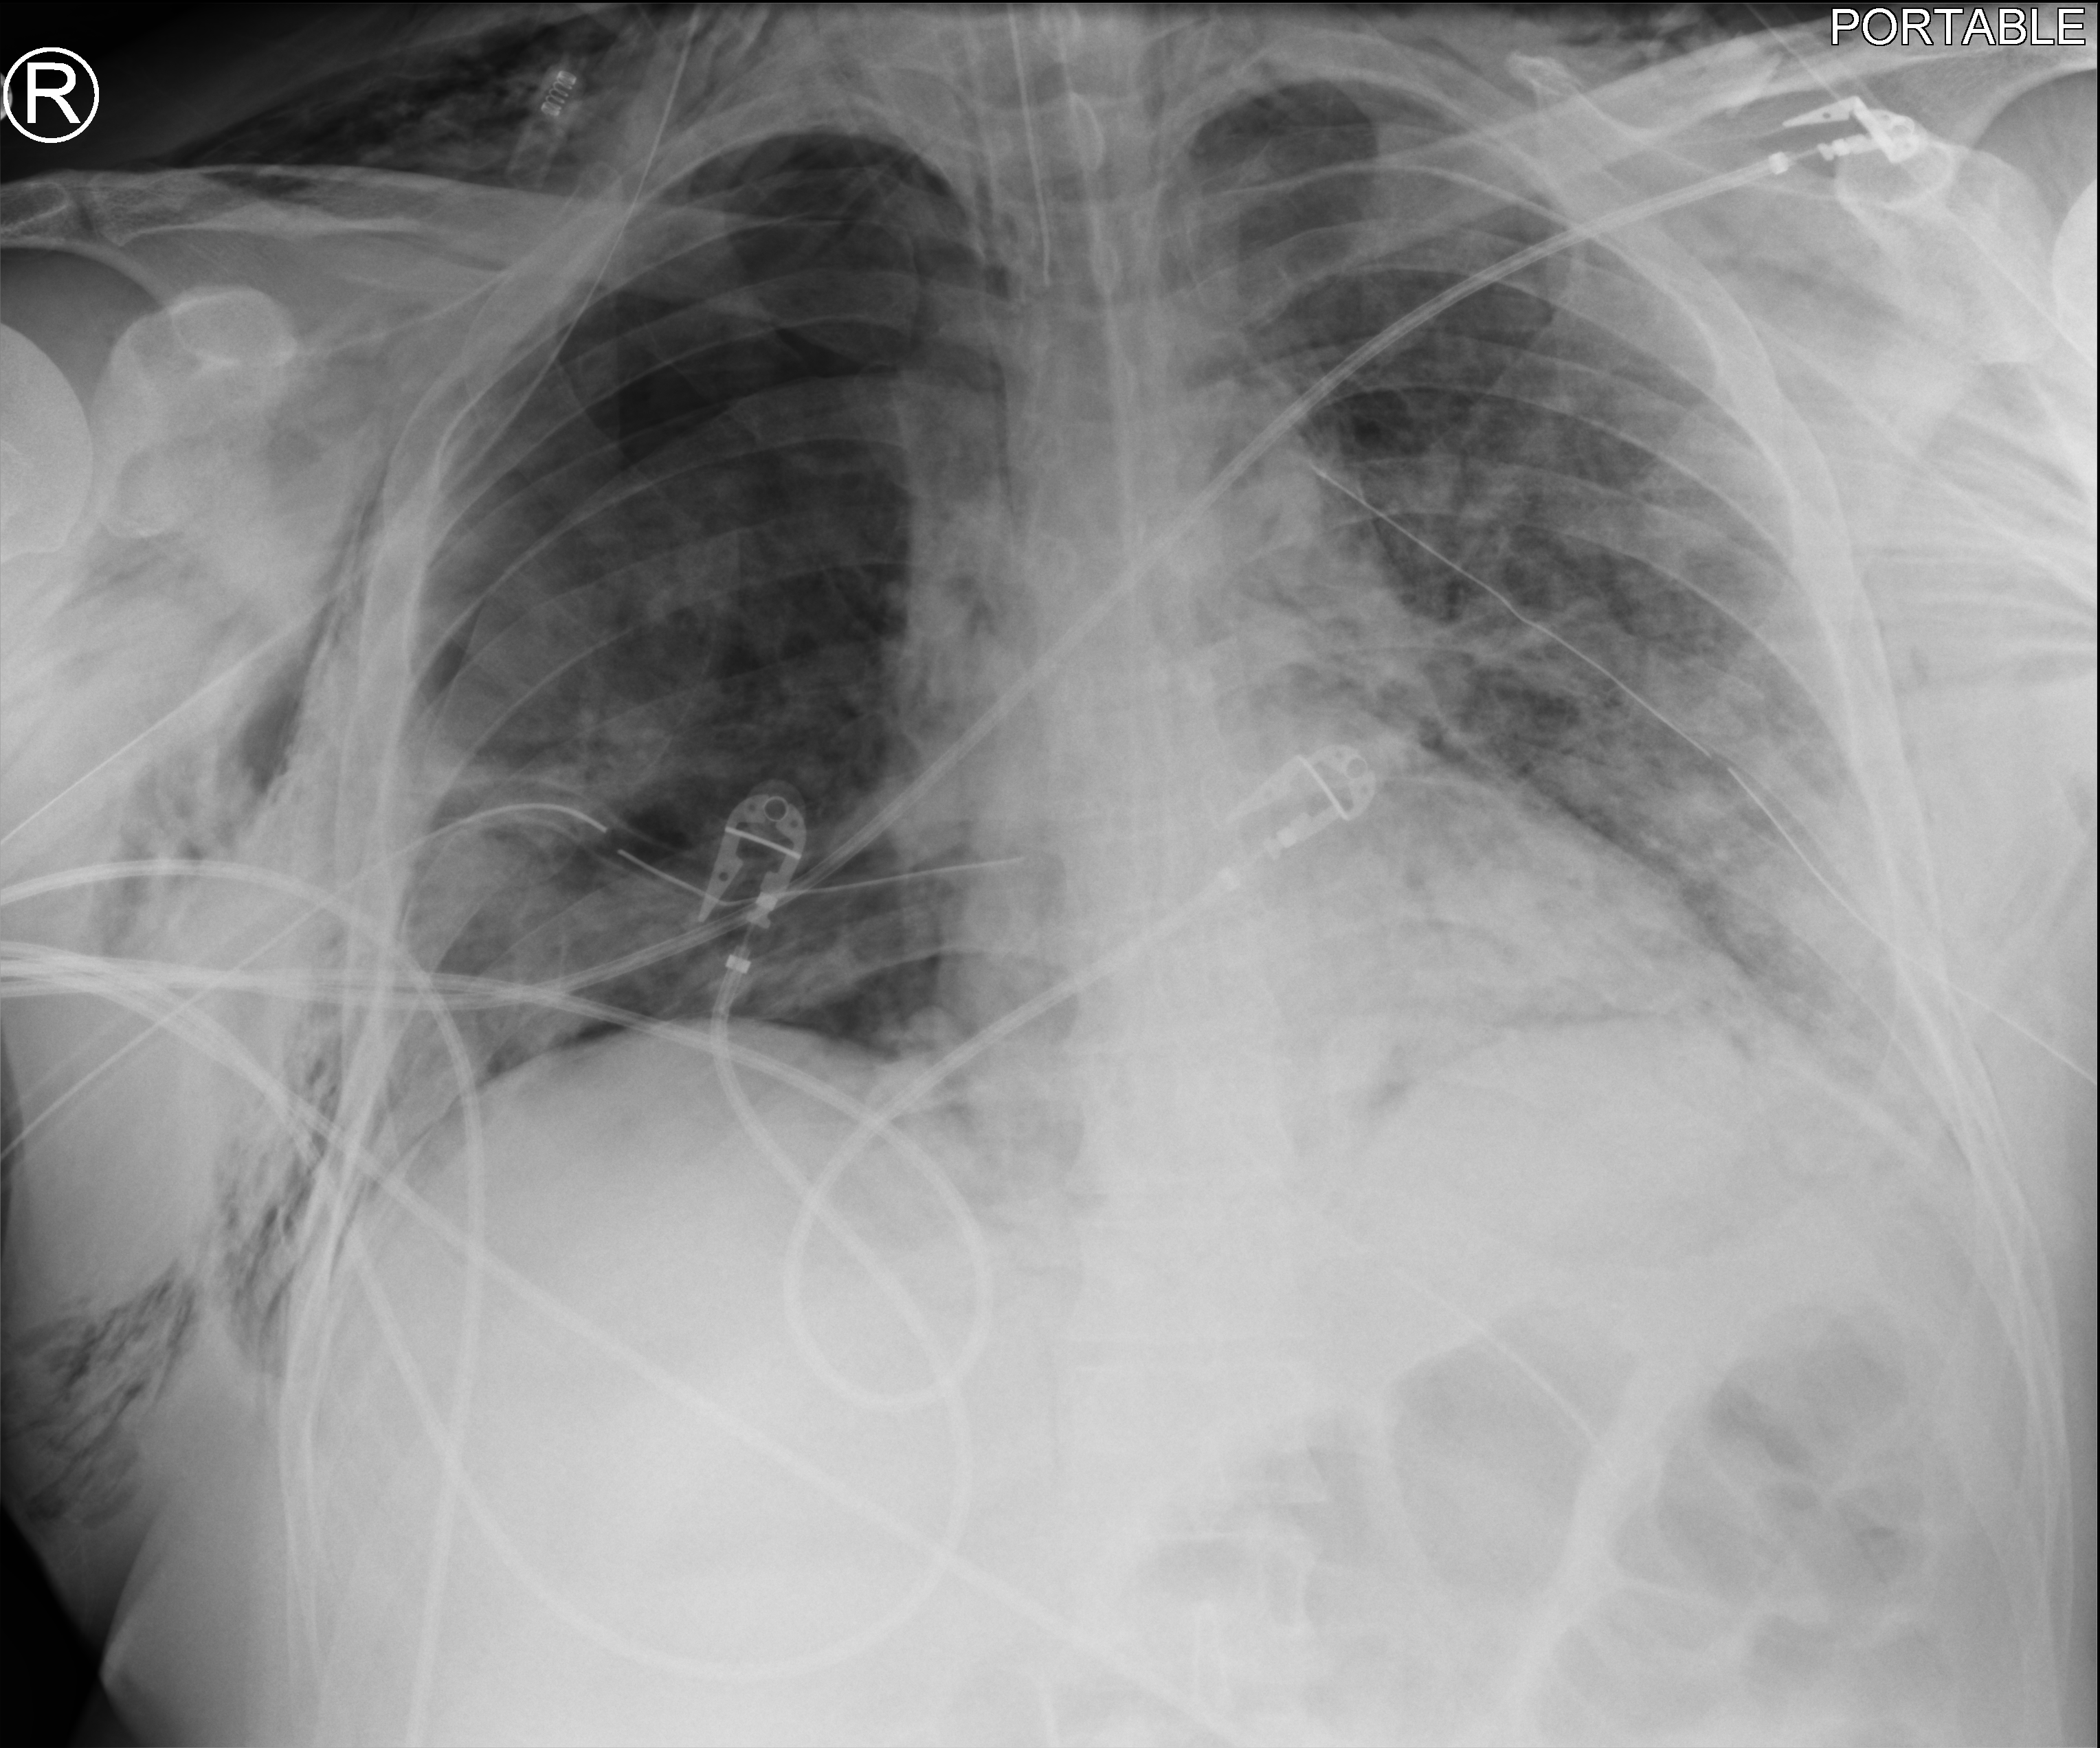
Chest X-ray (portable), anteroposterior (AP) projection. Patient hospitalised with COVID-19; male, aged 18–59 years.
Admission-level facts for this patient (not findings on this image; timing relative to this image not recorded):
- admitted to intensive care during this hospital stay: yes